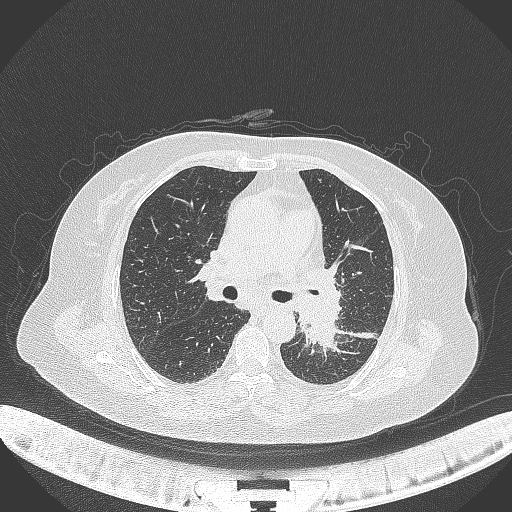
Chest CT, one axial slice. Slice 206 of 322 in the series (ordered by position). Lung window (W 1500 / L -600 HU). 1 mm slice thickness. 512 × 512 image matrix. Female patient, age 69 years. From the clinical record (not read from this slice): clinical TNM (as recorded): T2b N3 M1.
Structures marked on this image (rectangle marked by the reading radiologist):
- lung tumour (recorded histology: adenocarcinoma): bounding box (x1, y1, x2, y2) in pixels: (296, 300, 342, 355)